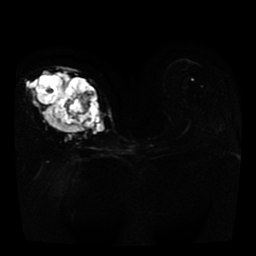
Breast MRI, one axial slice. Position 23 of 41 along the scan axis. Diffusion-weighted series; image 2 of 4 stored at this slice position (different b-values; order by instance number). 1.5 T. 5 mm slice thickness. 256 × 256 image matrix, field of view 330 × 330 mm. Female patient.
Annotated regions visible in this slice (outlined manually by an expert reader):
- tumour on diffusion-weighted imaging: bounding box (x1, y1, x2, y2) in pixels: (42, 72, 104, 131)